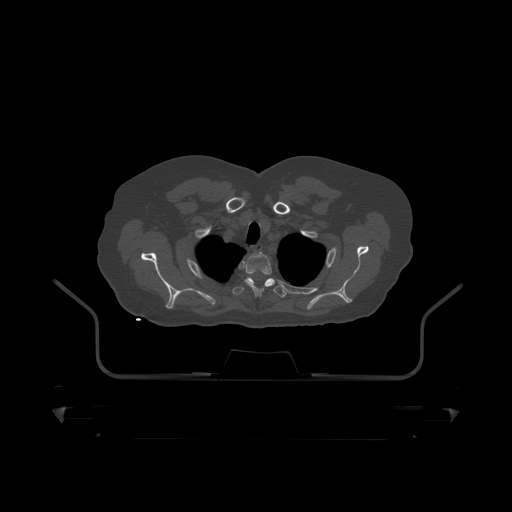
CT including the spine, one axial slice. Slice 370 of 390 in the series (ordered by position). Reconstruction kernel STANDARD. 120 kVp. Bone window (W 1800 / L 400 HU). 1.25 mm slice thickness. 512 × 512 image matrix, field of view 650 × 650 mm. Male patient, age 60 years. Case-level facts recorded for this patient, not image findings: primary cancer: prostate.
Outlined on this slice (semi-automatic segmentation, software-assisted and operator-edited):
- T1 vertebra: bounding box (x1, y1, x2, y2) in pixels: (242, 262, 245, 268)
- T2 vertebra: (246, 254, 273, 298)
- T3 vertebra: (233, 278, 287, 298)